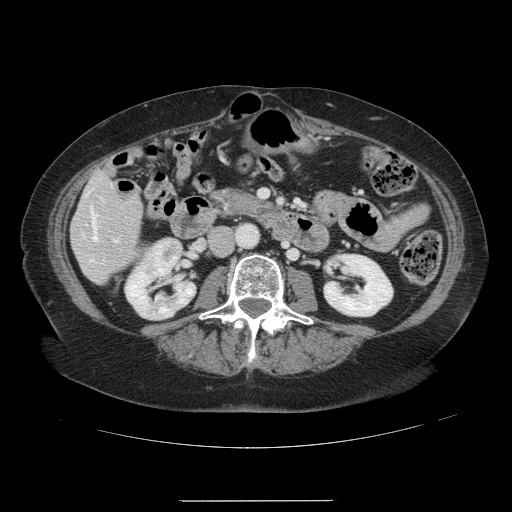
Contrast-enhanced abdominal CT, one axial slice. Slice 36 of 141 in the series (ordered by position). 120 kVp. Intravenous contrast given. Soft-tissue window (W 400 / L 40 HU). 512 × 512 image matrix, field of view 393 × 393 mm. Female patient, age 74 years. Case-level facts recorded for this patient, not image findings: diagnosis: colorectal cancer liver metastases, imaged before liver resection; multiple liver metastases: yes; largest metastasis: 7 cm; chemotherapy before resection: no.
Annotated regions visible in this slice (manually delineated by an expert):
- hepatic veins: bounding box <91,209,97,240> (left, top, right, bottom; pixels)
- liver: <72,173,142,283>
- planned liver remnant (the part of the liver to remain after resection): <75,173,142,283>
- portal vein (with intrahepatic branches): <114,239,117,242>